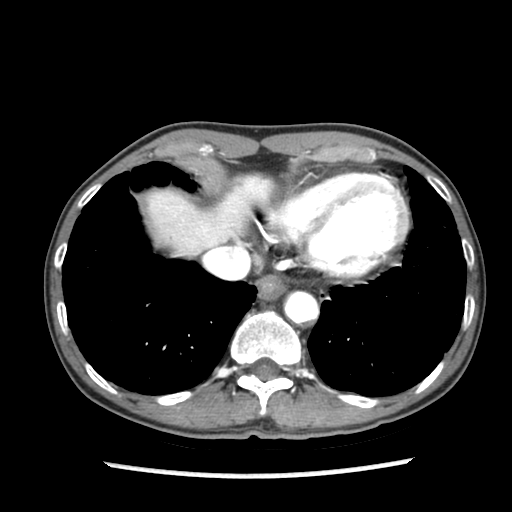
Contrast-enhanced abdominal CT (liver protocol), one axial slice. Slice 74 of 87 in the series (ordered by position). Reconstruction kernel STANDARD. 140 kVp. Soft-tissue window (W 400 / L 40 HU). 2.5 mm slice thickness. 512 × 512 image matrix, field of view 300 × 300 mm. From the clinical record (not read from this slice): diagnosis: hepatocellular carcinoma (patient treated with transarterial chemoembolisation; whether this scan precedes or follows treatment is not stated here); TNM stage (as recorded): Stage-IIIB; Child-Pugh class: A; tumour differentiation: well differentiated; tumour nodularity: uninodular.
Annotated regions visible in this slice (semi-automatic segmentation, software-assisted and operator-edited):
- abdominal aorta: bounding box (x1, y1, x2, y2) in pixels: (286, 293, 317, 321)
- liver parenchyma outside the tumour (the mass and vessels are separate outlines, so this box may not span the whole liver): (148, 178, 270, 254)